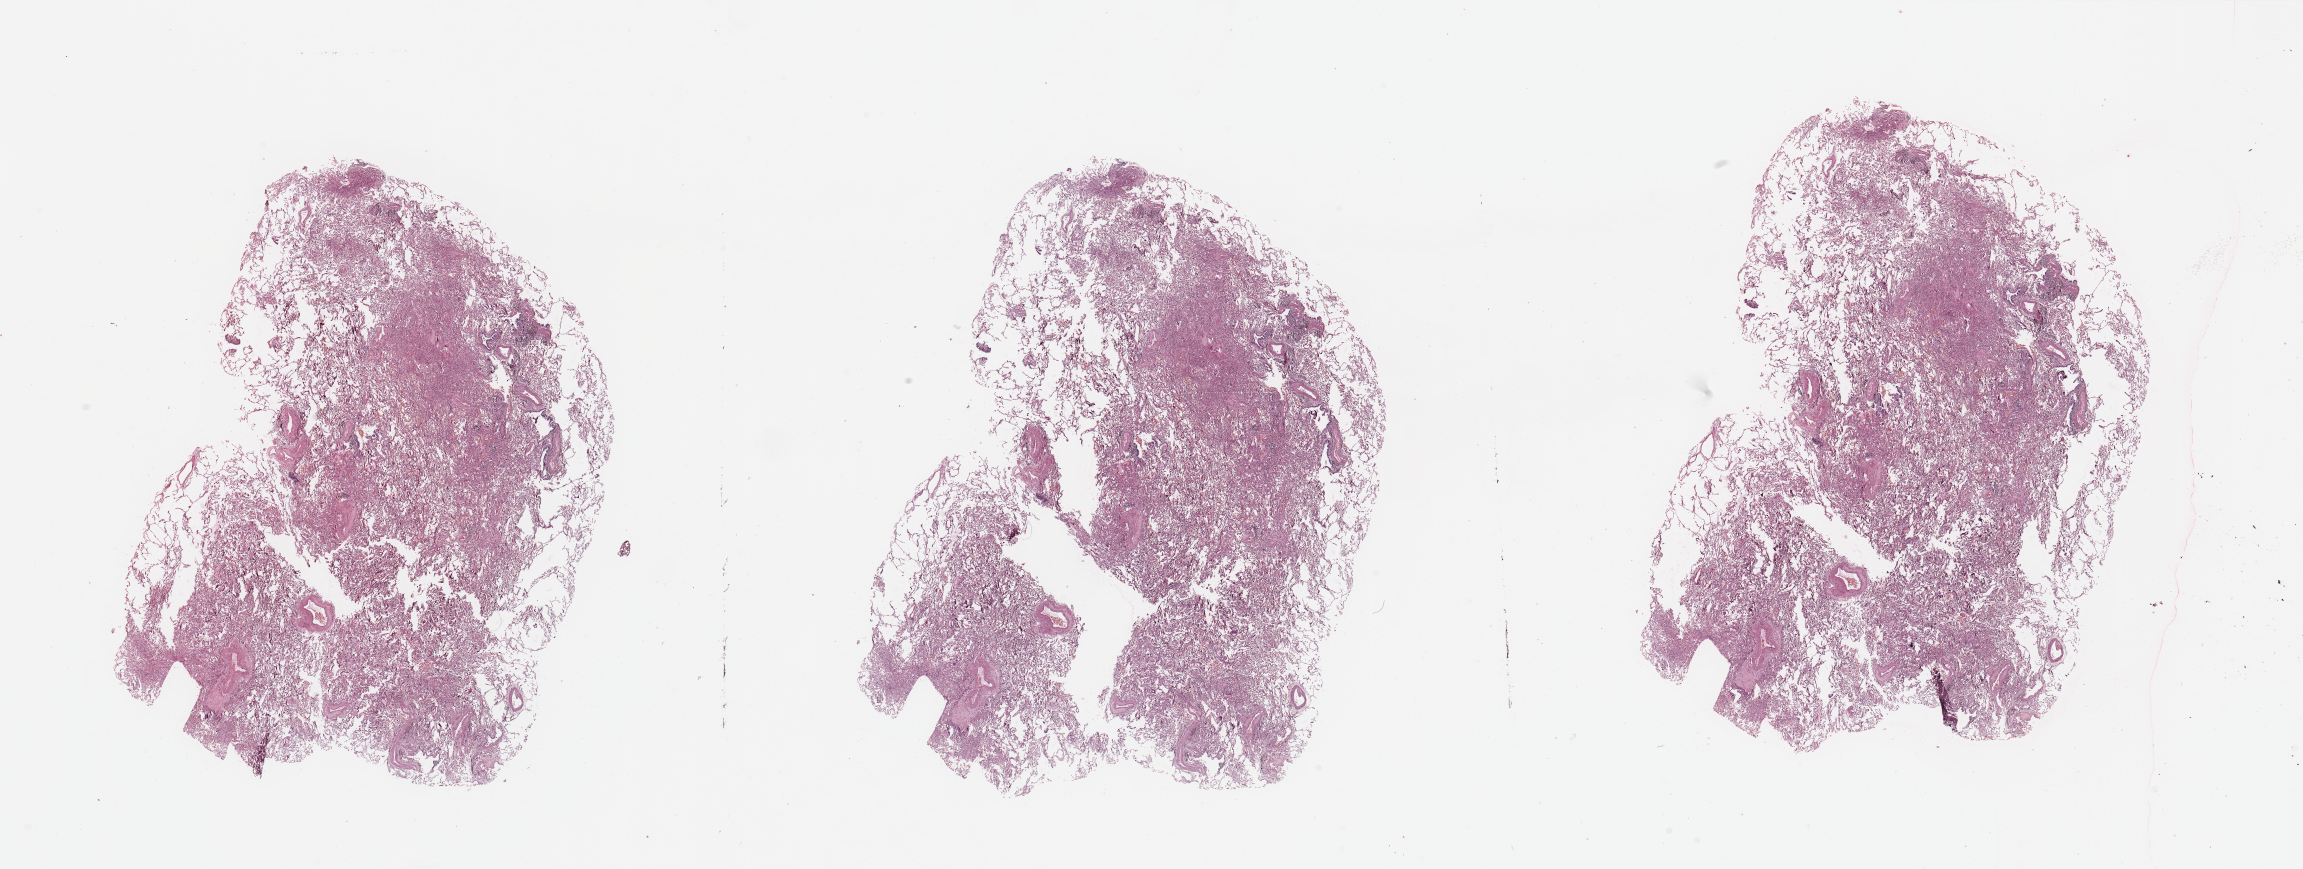
Whole-slide histology image, Hematoxylin and eosin (H&E) stained — low-resolution overview of the scanned area, about 36.4 x 13.7 mm (from a 20x scan). Normal (non-tumour) tissue sample, lung. Female, 73 y/o.
This section: normal (non-tumour) tissue from the same patient. Patient diagnosis: Adenocarcinoma, NOS.